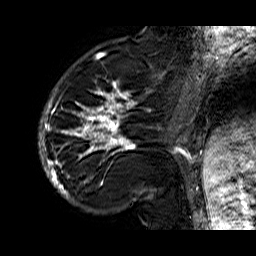
Breast MRI (dynamic contrast-enhanced), one sagittal slice; slice 16 of 60 in the series (ordered by position); dynamic contrast-enhanced series, time point 2 of 6 at this slice position (early post-contrast); 1.5 T; TE 6.3 ms, TR 32.9 ms; 4 mm slice thickness; 256 × 256 image matrix, field of view 200 × 200 mm. Female patient. From the clinical record (not read from this slice): setting: breast cancer imaged before/during neoadjuvant chemotherapy; receptor status: HR-positive, HER2-negative.
Annotated regions visible in this slice (semi-automatically segmented with operator editing):
- analysis volume of interest (the breast-tissue region the enhancement analysis was run in; not a lesion): bounding box (x1, y1, x2, y2) in pixels: (39, 74, 176, 210)
- tumour enhancement mask (voxels above the 100 % enhancement threshold inside the analysis volume of interest): (39, 74, 176, 201)